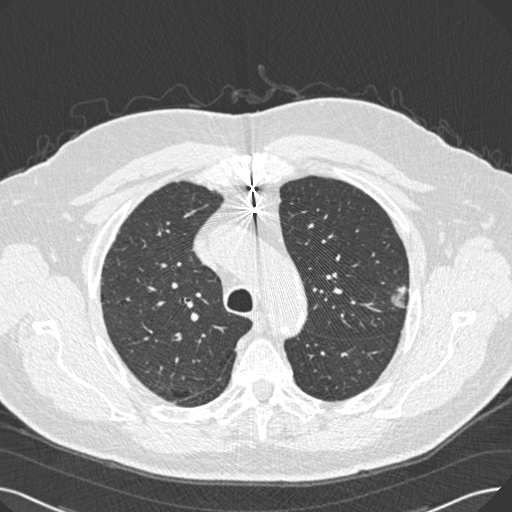
Low-dose screening chest CT, one axial slice. Position 197 of 269 along the scan axis. Lung window (W 1500 / L -600 HU). 1 mm slice thickness. 512 × 512 image matrix, field of view 370 × 370 mm.
Outlined on this slice (manually delineated by an expert):
- lesion 1 (tumor, upper lobe of left lung): bounding box <392,286,407,308> (left, top, right, bottom; pixels)